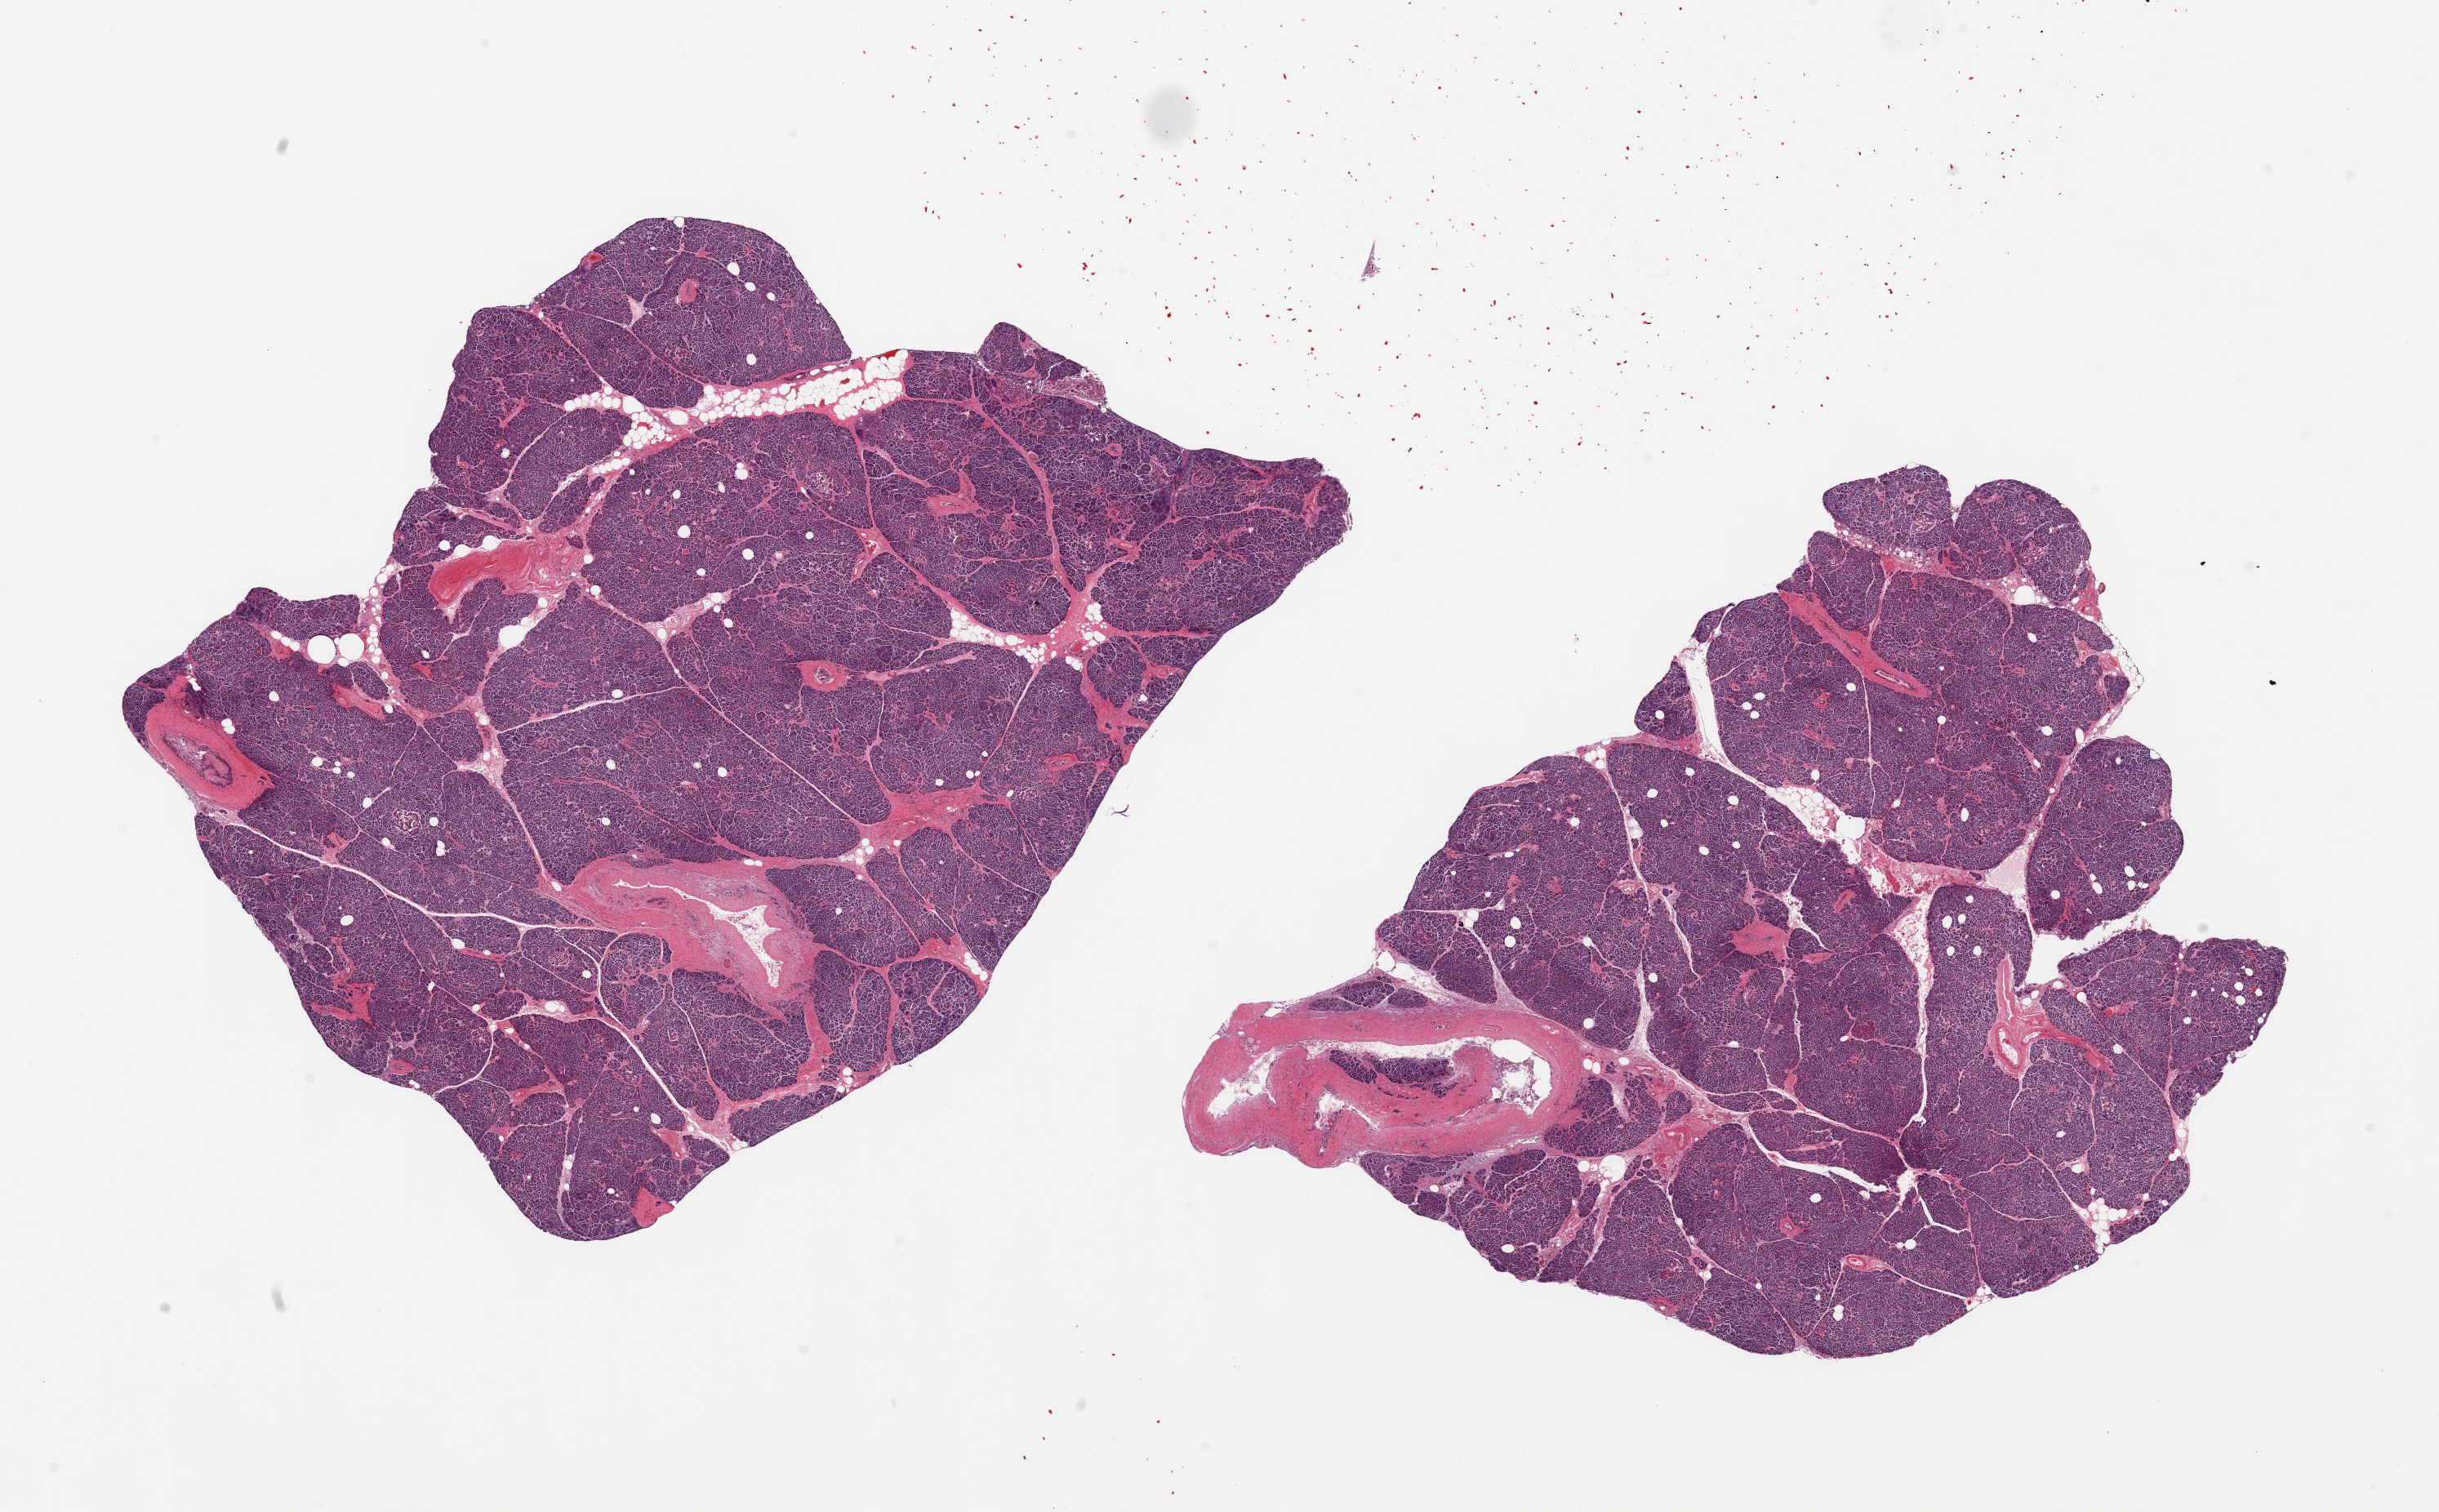
Whole-slide image, H&E stain — shown as a low-resolution overview of the whole scanned area (about 23.6 x 14.6 mm, slide scanned at 20x). PAXgene-fixed paraffin-embedded (PFPE) section. Target tissue: pancreas. Donor tissue sample.
- review note (as recorded): 2 pieces; sloughing ductal epithelium; residual islets